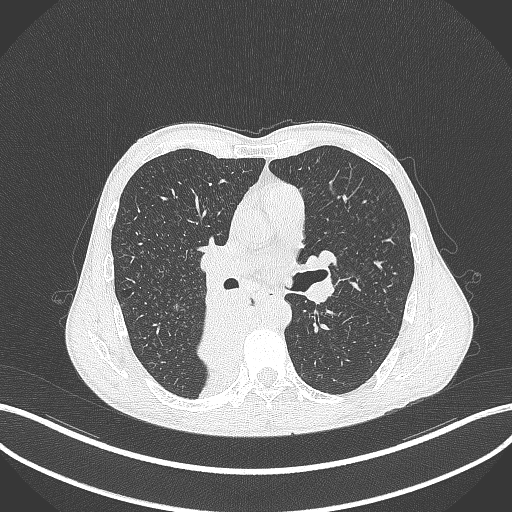
Chest CT, one axial slice; slice 214 of 371 in the series (ordered by position); 120 kVp; lung window (W 1500 / L -600 HU); 1 mm slice thickness; 512 × 512 image matrix. Patient: male, 58 years. From the clinical record (not read from this slice): clinical TNM (as recorded): T3 N1 M1.
Outlined on this slice (rectangle marked by the reading radiologist):
- lung tumour (recorded histology: squamous cell carcinoma): box from (x=190, y=295) to (x=264, y=389) px